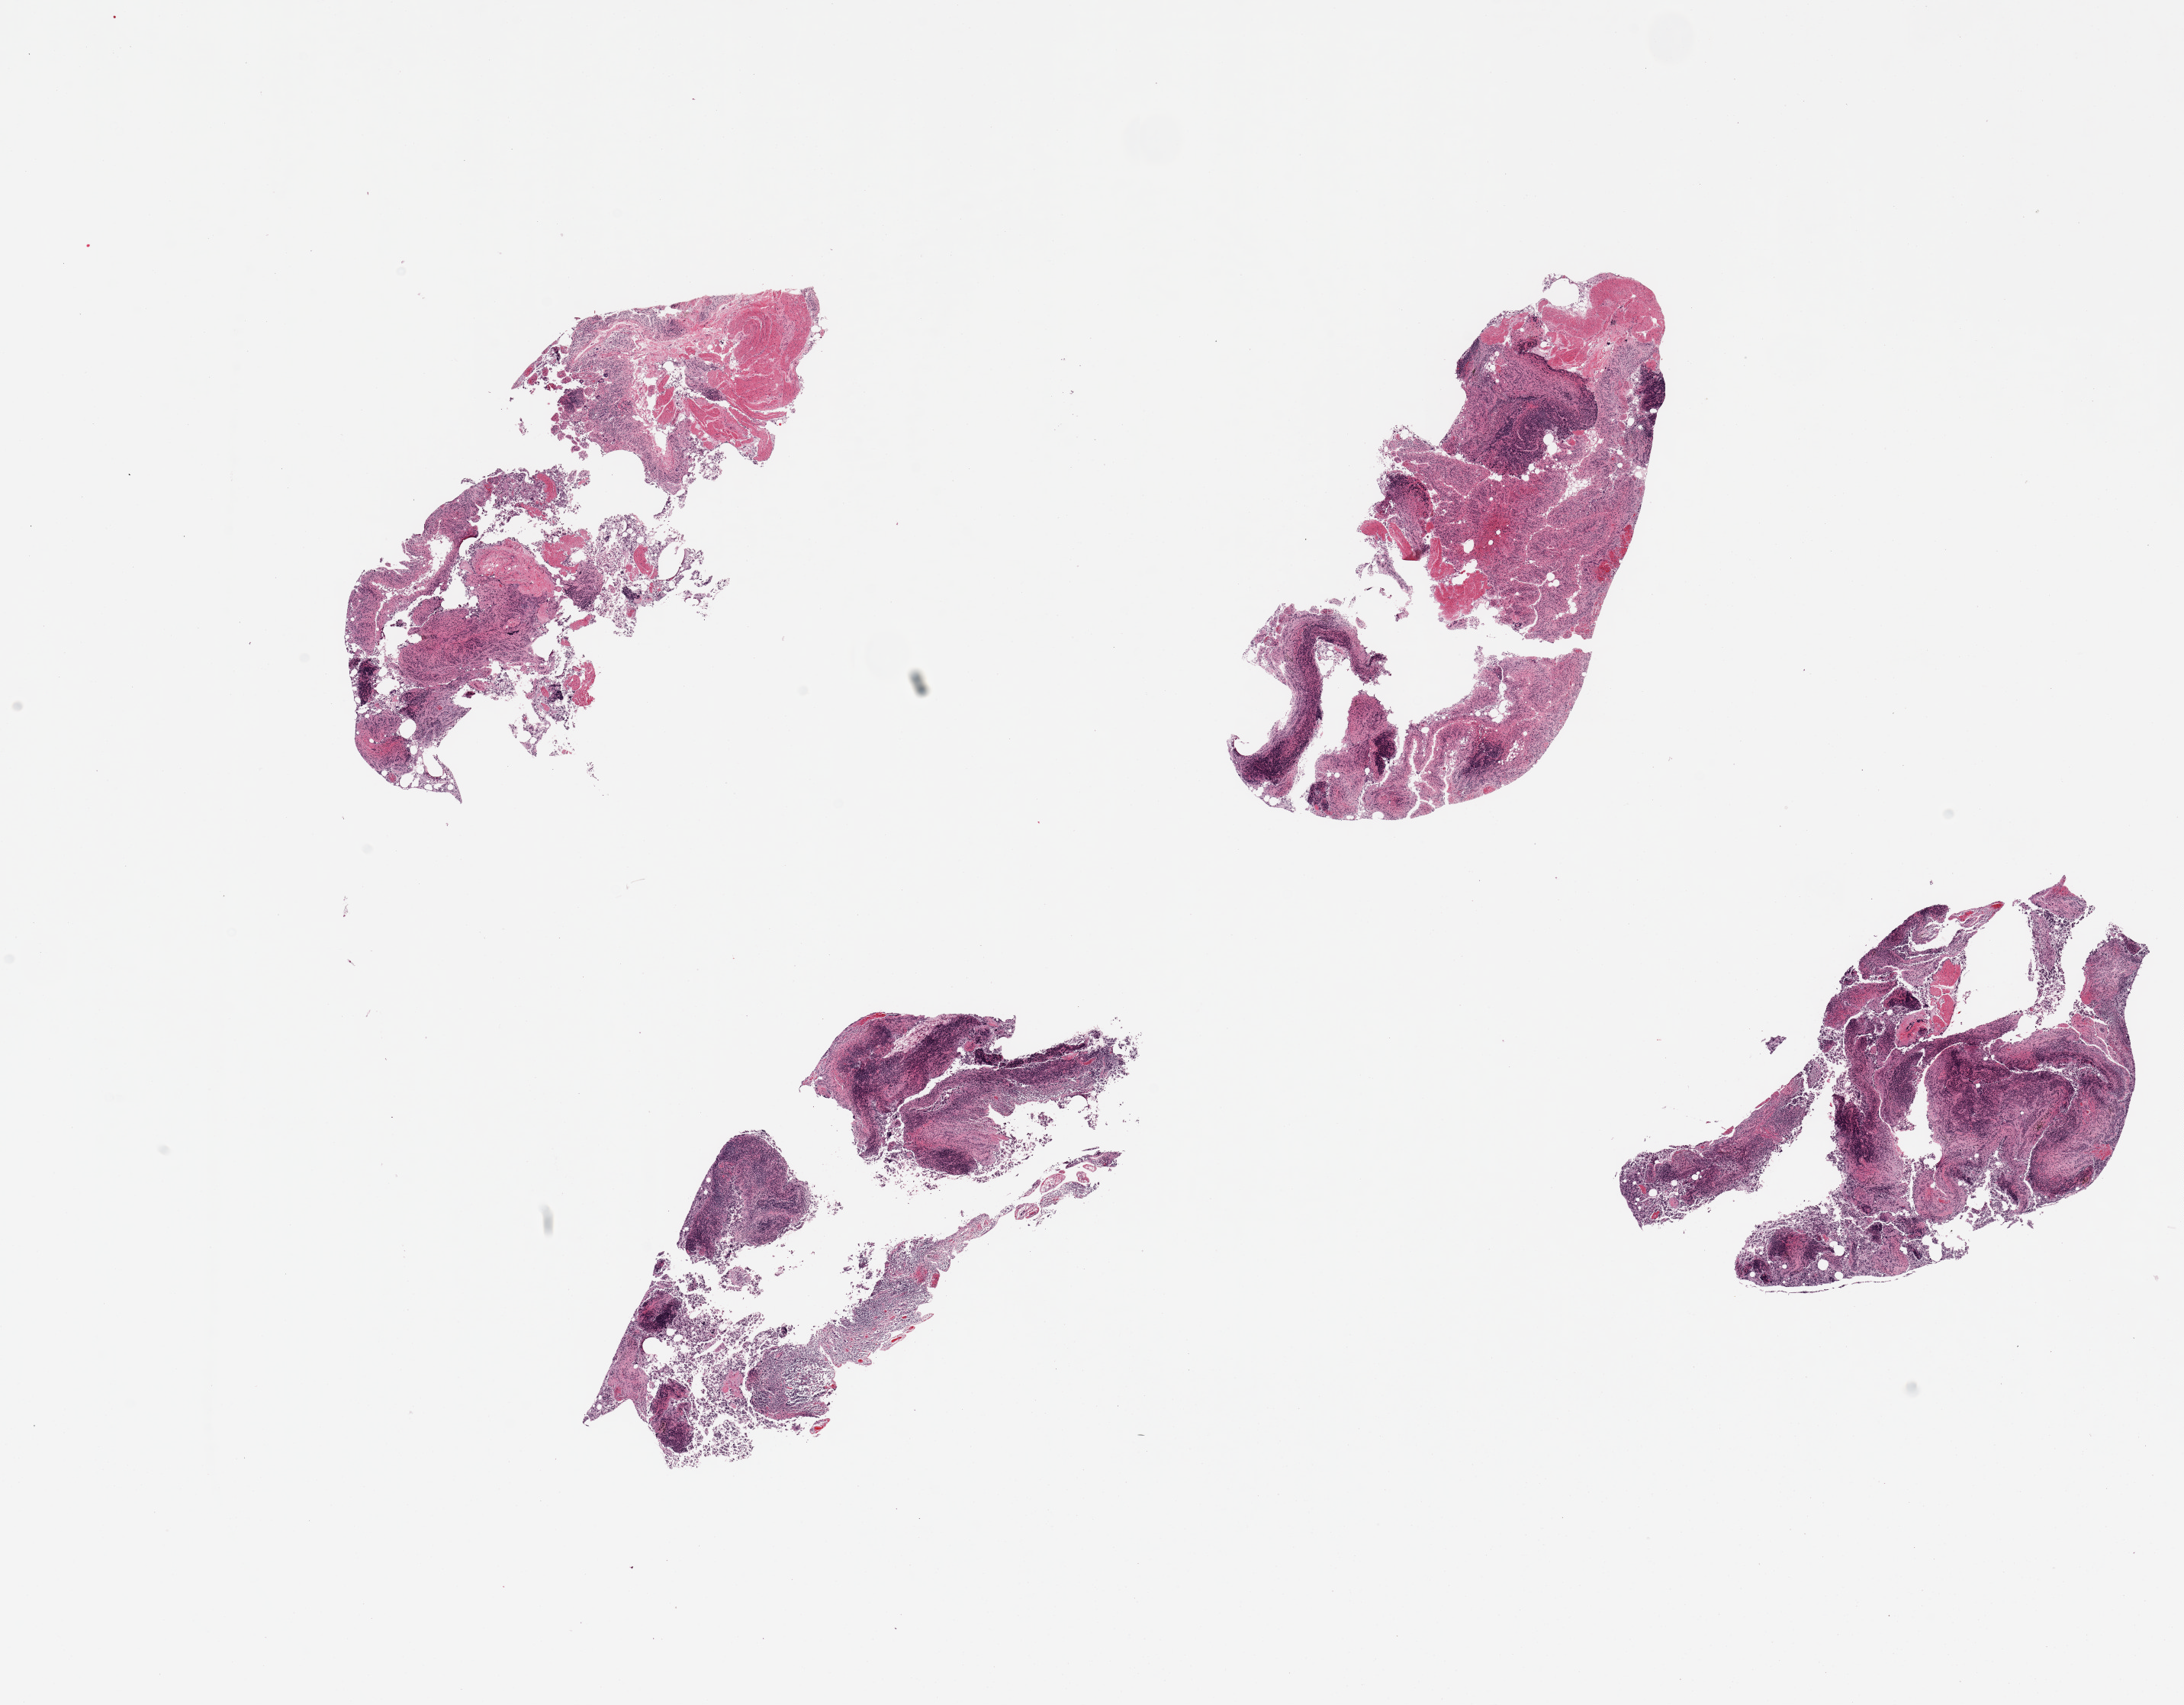
Hematoxylin and eosin (H&E) whole-slide image, a low-resolution overview of the entire scanned area, about 22.6 x 17.7 mm; PAXgene-fixed paraffin-embedded (PFPE) section; sampled site (target tissue): ileum; tissue donor sample.
- pathologist's review note for this sample: 4 pieces, fragmented pieces of muscularis and autolyzed mucosa with lymphoid component